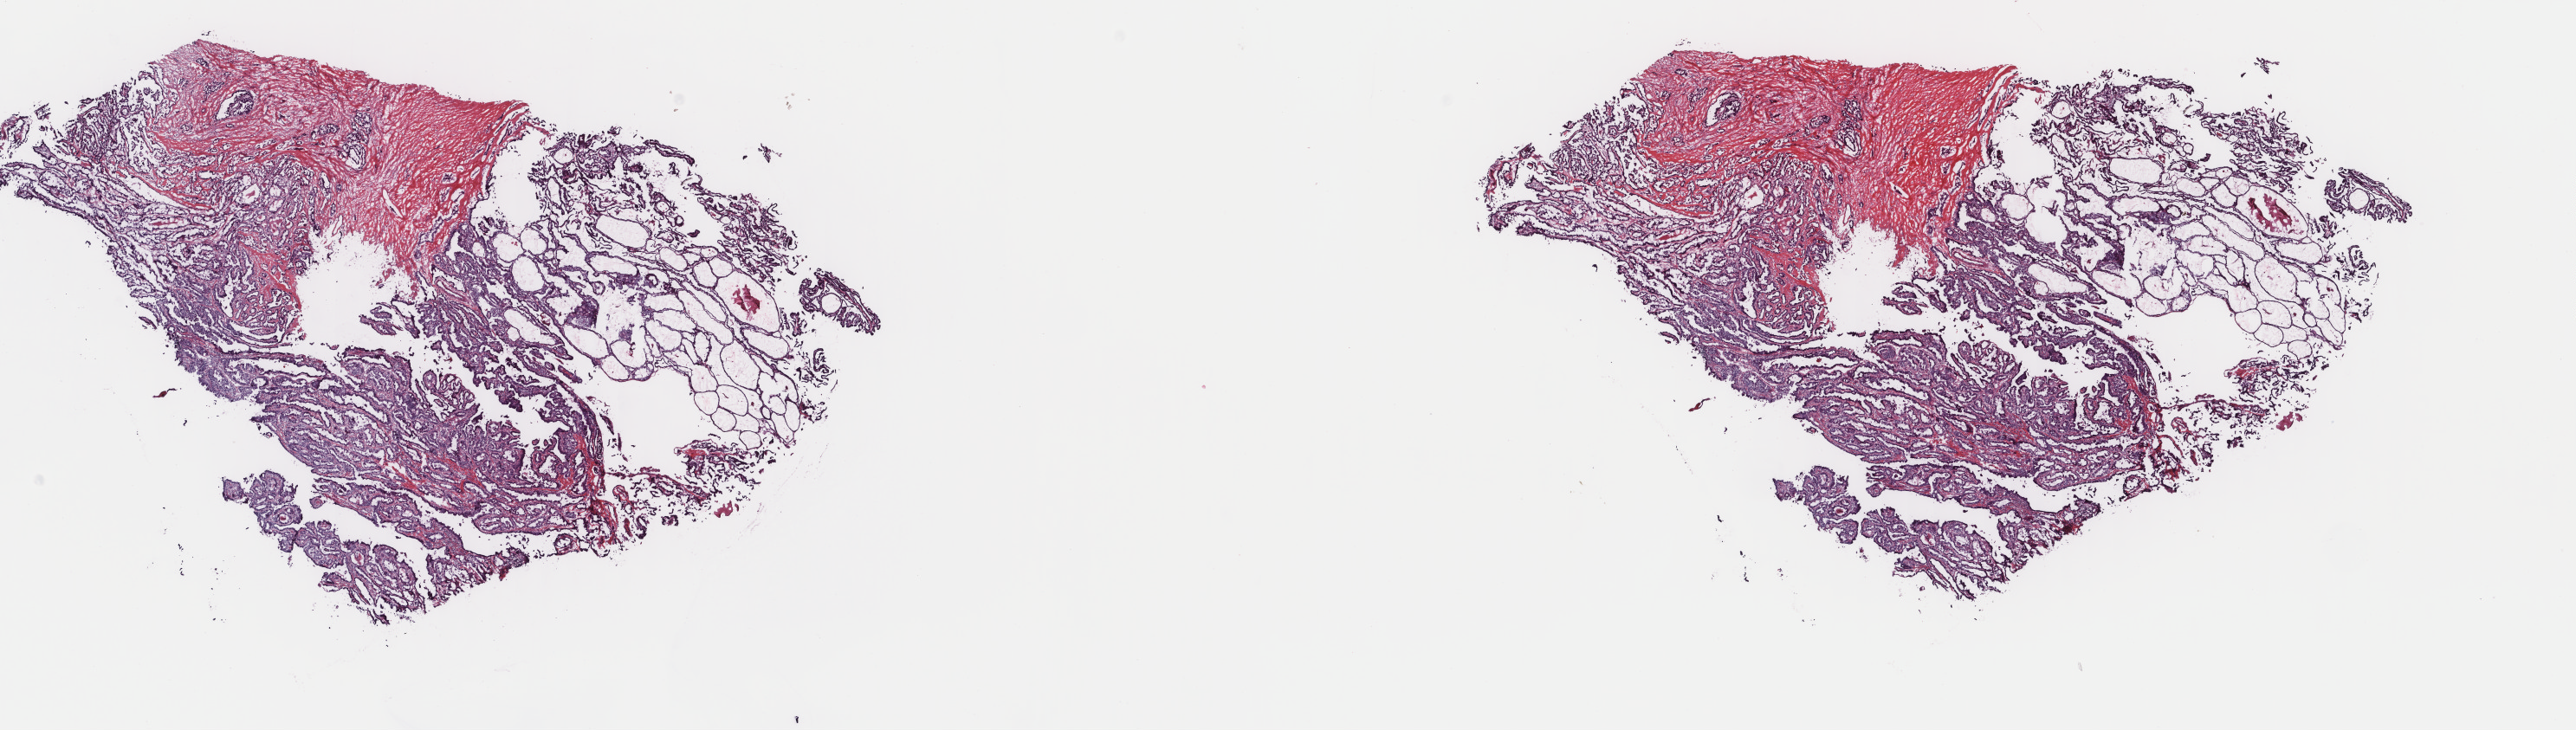
H&E-stained whole-slide image — whole scanned area (about 23.6 x 6.7 mm, acquisition: 40x scan) shown as a low-resolution overview; frozen section from the top of the tissue portion; sample: primary tumour, thyroid. Patient: female, age at initial diagnosis 42 years. Slide review estimates, as recorded: tumour cells 75%, tumour nuclei 80%, normal cells 0%, stromal cells 25%, necrosis 0%. Infiltration values recorded for this section: lymphocyte infiltration 2%, monocyte infiltration 0%, neutrophil infiltration 0%.
Lymph nodes positive (case pathology): 4 of 18 examined. AJCC pathologic stage: I (7th edition). Pathologic diagnosis: Nonencapsulated sclerosing carcinoma (thyroid gland). Laterality: bilateral.